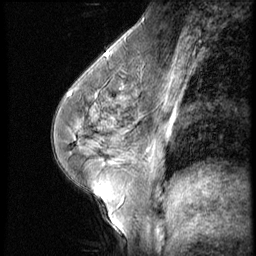
Breast MRI (dynamic contrast-enhanced), one sagittal slice. Position 29 of 56 along the scan axis. 3 images stored at this slice position (order not interpretable as contrast timing). 1.5 T. TE 4.2 ms, TR 9 ms. 256 × 256 image matrix. Patient: female, 45 years. Case-level facts recorded for this patient, not image findings: setting: breast cancer imaged before/during neoadjuvant chemotherapy; receptor status: HR-positive, HER2-negative.
Annotated regions visible in this slice (semi-automatically segmented with operator editing):
- analysis volume of interest (the breast-tissue region the enhancement analysis was run in; not a lesion): bounding box (x1, y1, x2, y2) in pixels: (102, 77, 166, 129)
- tumour enhancement mask (voxels above the 140 % enhancement threshold inside the analysis volume of interest): (109, 83, 132, 128)